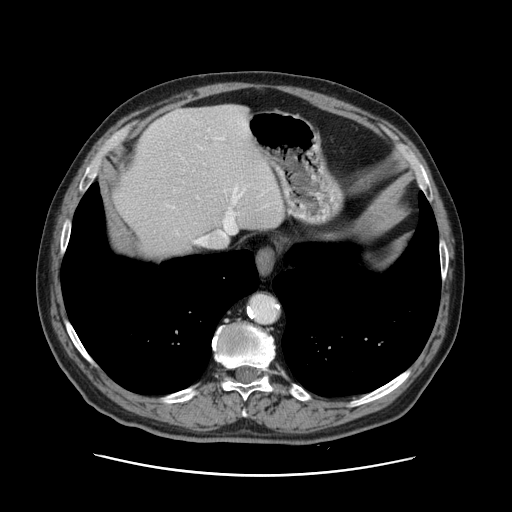
Contrast-enhanced abdominal CT, one axial slice; position 110 of 141 along the scan axis; soft-tissue window (W 400 / L 40 HU); 2.5 mm slice thickness; 512 × 512 image matrix, field of view 395 × 395 mm. Male patient, age 72 years. Case-level facts recorded for this patient, not image findings: diagnosis: colorectal cancer liver metastases, imaged before liver resection; multiple liver metastases: yes; largest metastasis: 5.4 cm; disease in both lobes: yes.
Annotated regions visible in this slice (outlined manually by an expert reader):
- hepatic veins: bounding box (x1, y1, x2, y2) in pixels: (172, 129, 244, 246)
- liver: (114, 105, 284, 256)
- planned liver remnant (the part of the liver to remain after resection): (147, 105, 284, 256)